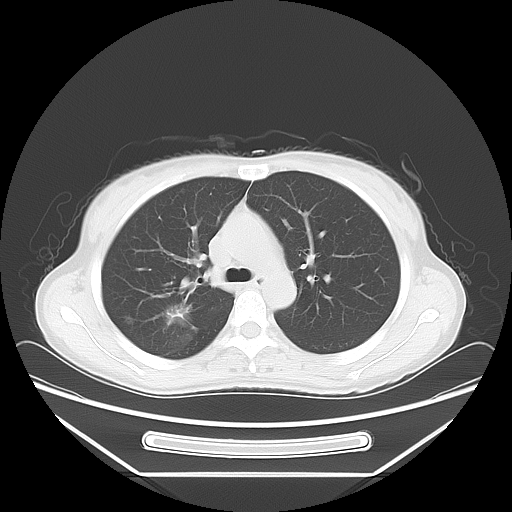
Chest CT, one axial slice; position 46 of 66 along the scan axis; 120 kVp; lung window (W 1500 / L -600 HU); 5 mm slice thickness; 512 × 512 image matrix. Patient: female, 37 years. Case-level facts recorded for this patient, not image findings: clinical TNM (as recorded): T1c N0 M1.
Outlined on this slice (rectangle marked by the reading radiologist):
- lung tumour (recorded histology: adenocarcinoma): box from (x=163, y=302) to (x=201, y=327) px